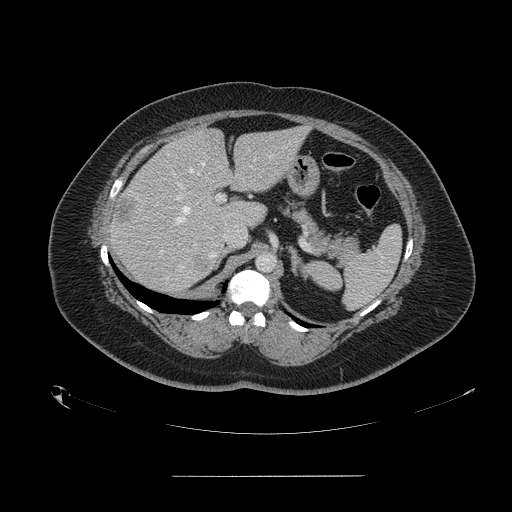
Contrast-enhanced abdominal CT, one axial slice. Slice 98 of 164 in the series (ordered by position). Intravenous contrast given. Soft-tissue window (W 400 / L 40 HU). 2.5 mm slice thickness. 512 × 512 image matrix. Female patient, age 52 years. Case-level facts recorded for this patient, not image findings: diagnosis: colorectal cancer liver metastases, imaged before liver resection; multiple liver metastases: yes; largest metastasis: 3.5 cm; disease in both lobes: no.
Structures marked on this image (manually delineated by an expert):
- hepatic veins: box from (x=175, y=162) to (x=204, y=224) px
- liver: (x=111, y=129)–(x=306, y=293)
- planned liver remnant (the part of the liver to remain after resection): (x=175, y=128)–(x=306, y=228)
- portal vein (with intrahepatic branches): (x=172, y=172)–(x=226, y=202)
- liver metastasis: (x=192, y=254)–(x=209, y=272)
- liver metastasis: (x=115, y=199)–(x=134, y=227)